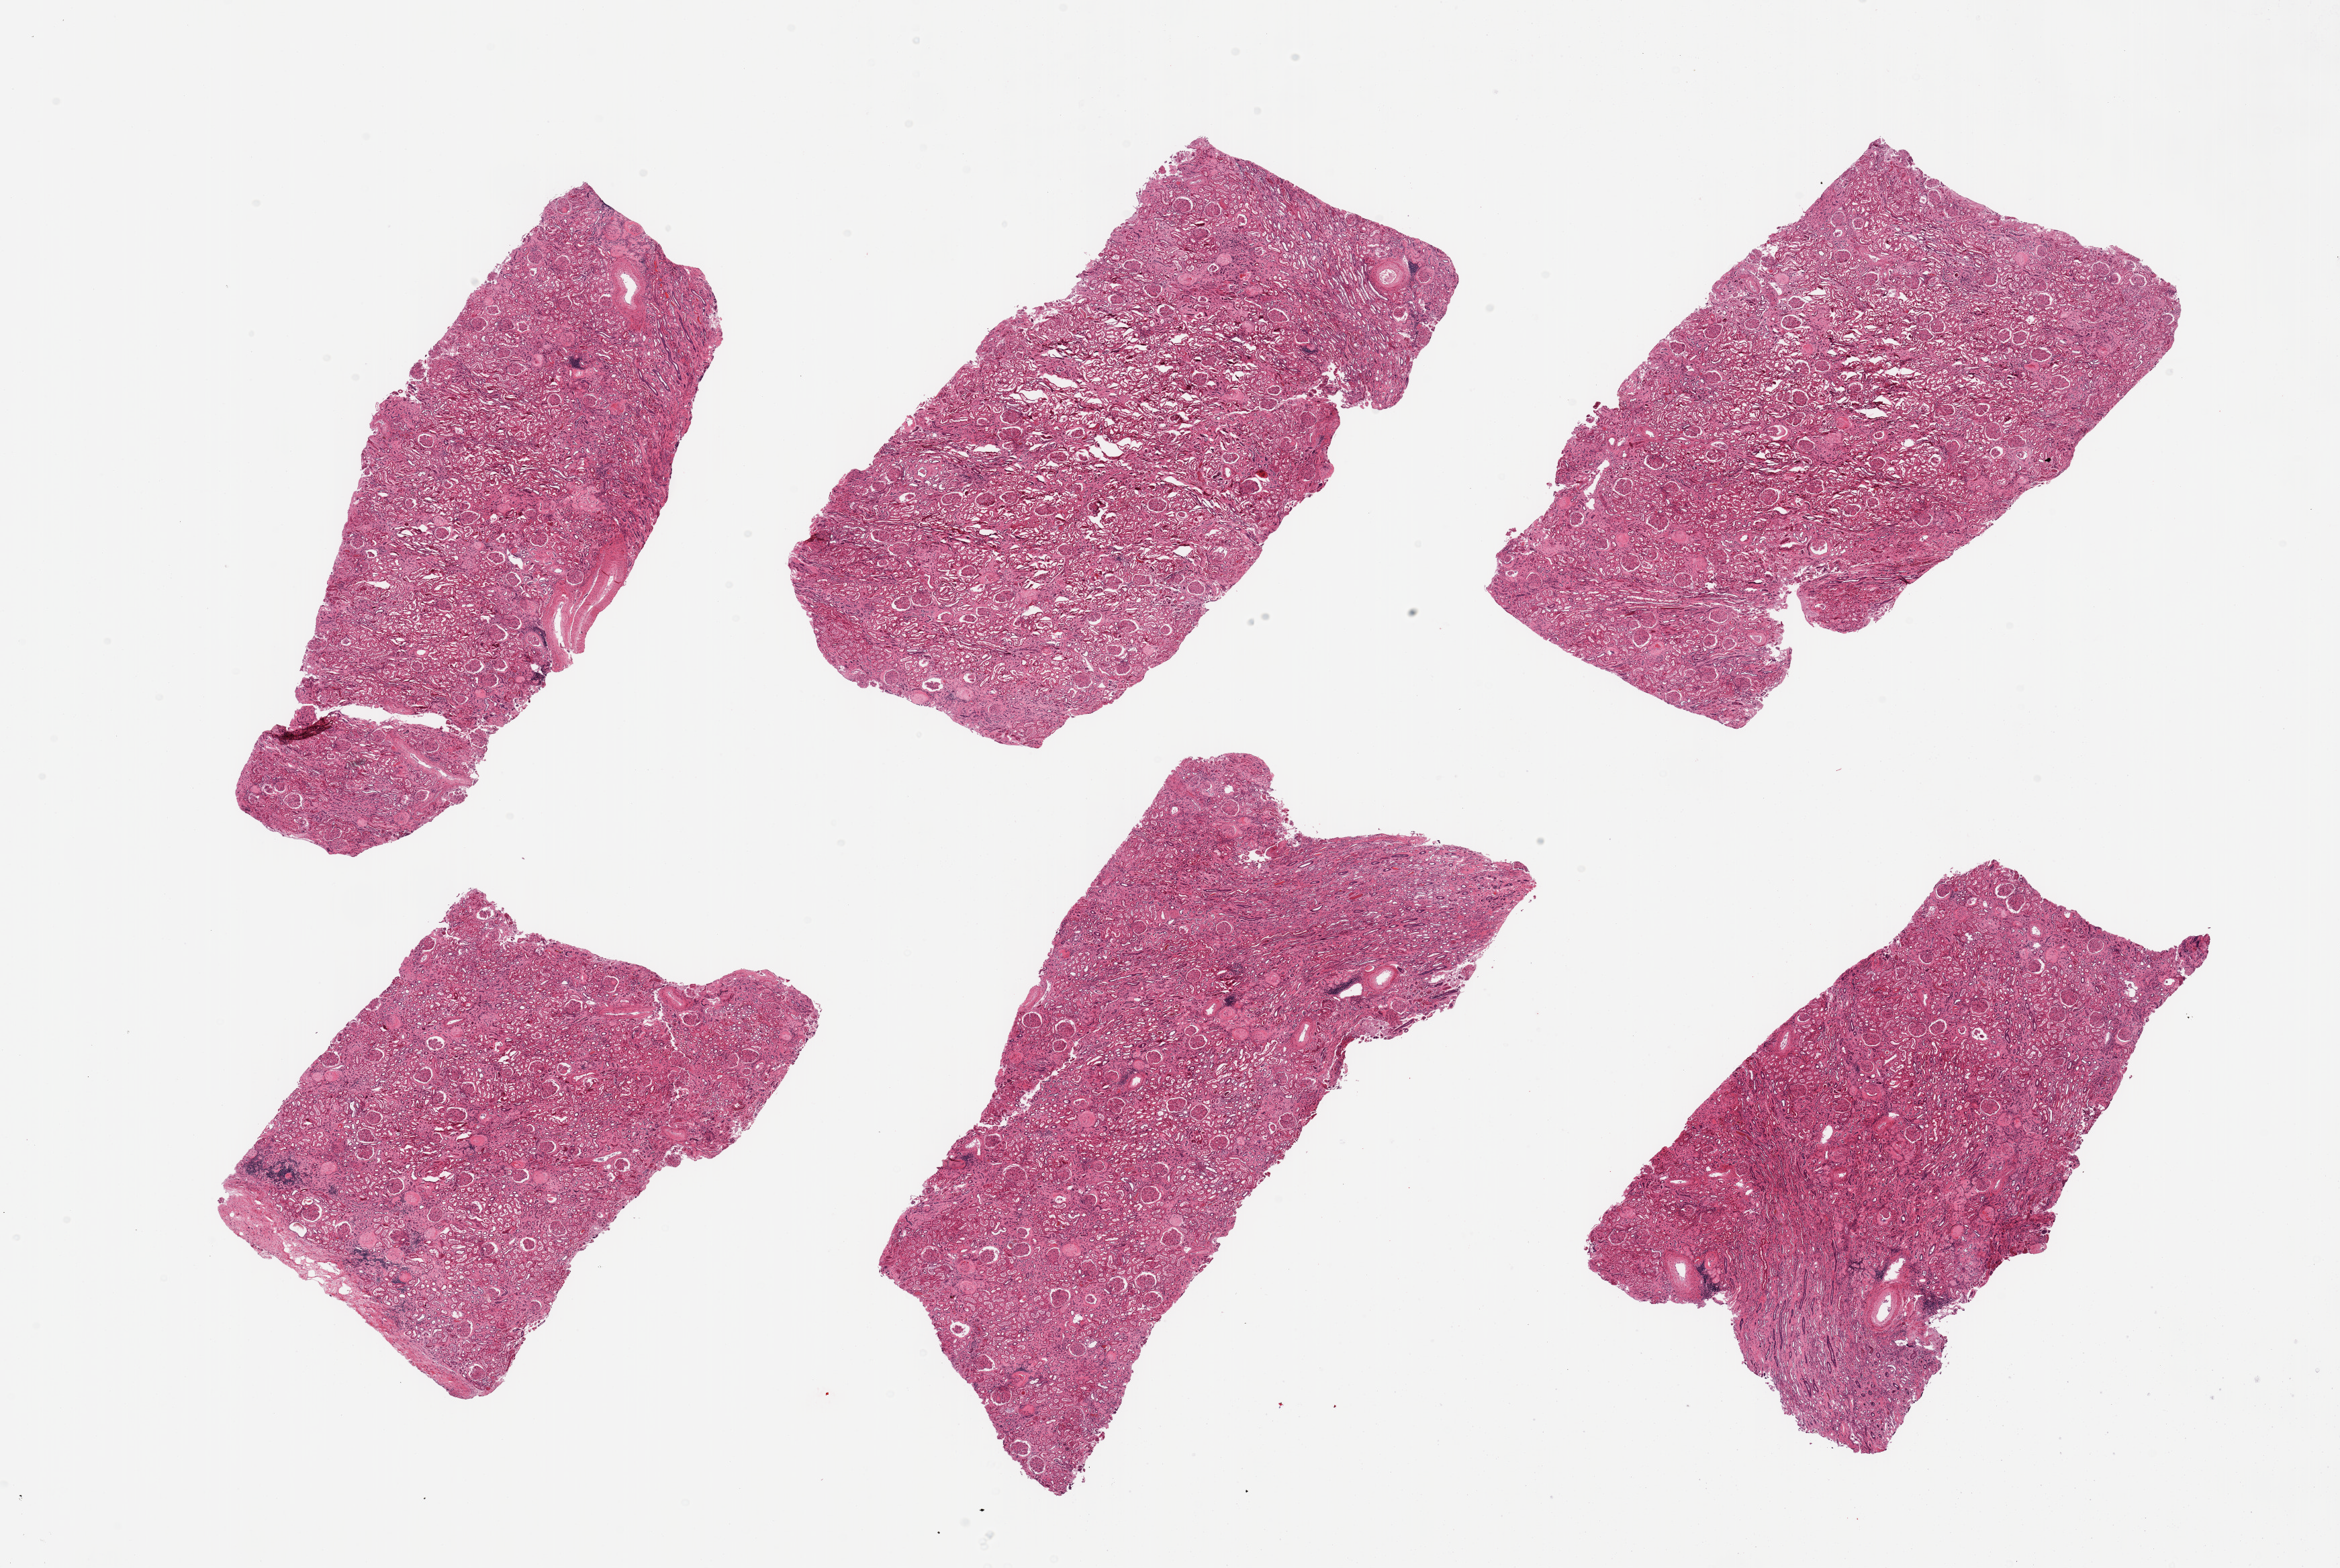
Whole-slide image, H&E stain, brightfield — low-resolution overview of the scanned area, about 27.6 x 18.5 mm. PAXgene-fixed, paraffin-embedded tissue. Section of renal cortex (target tissue). Tissue donor sample. Donor: male.
• reviewer comment on this tissue sample: 6 pieces; severe arteriolar and glomerular sclerosis with diabetic-type 'cannon-ball' glomerular lesions